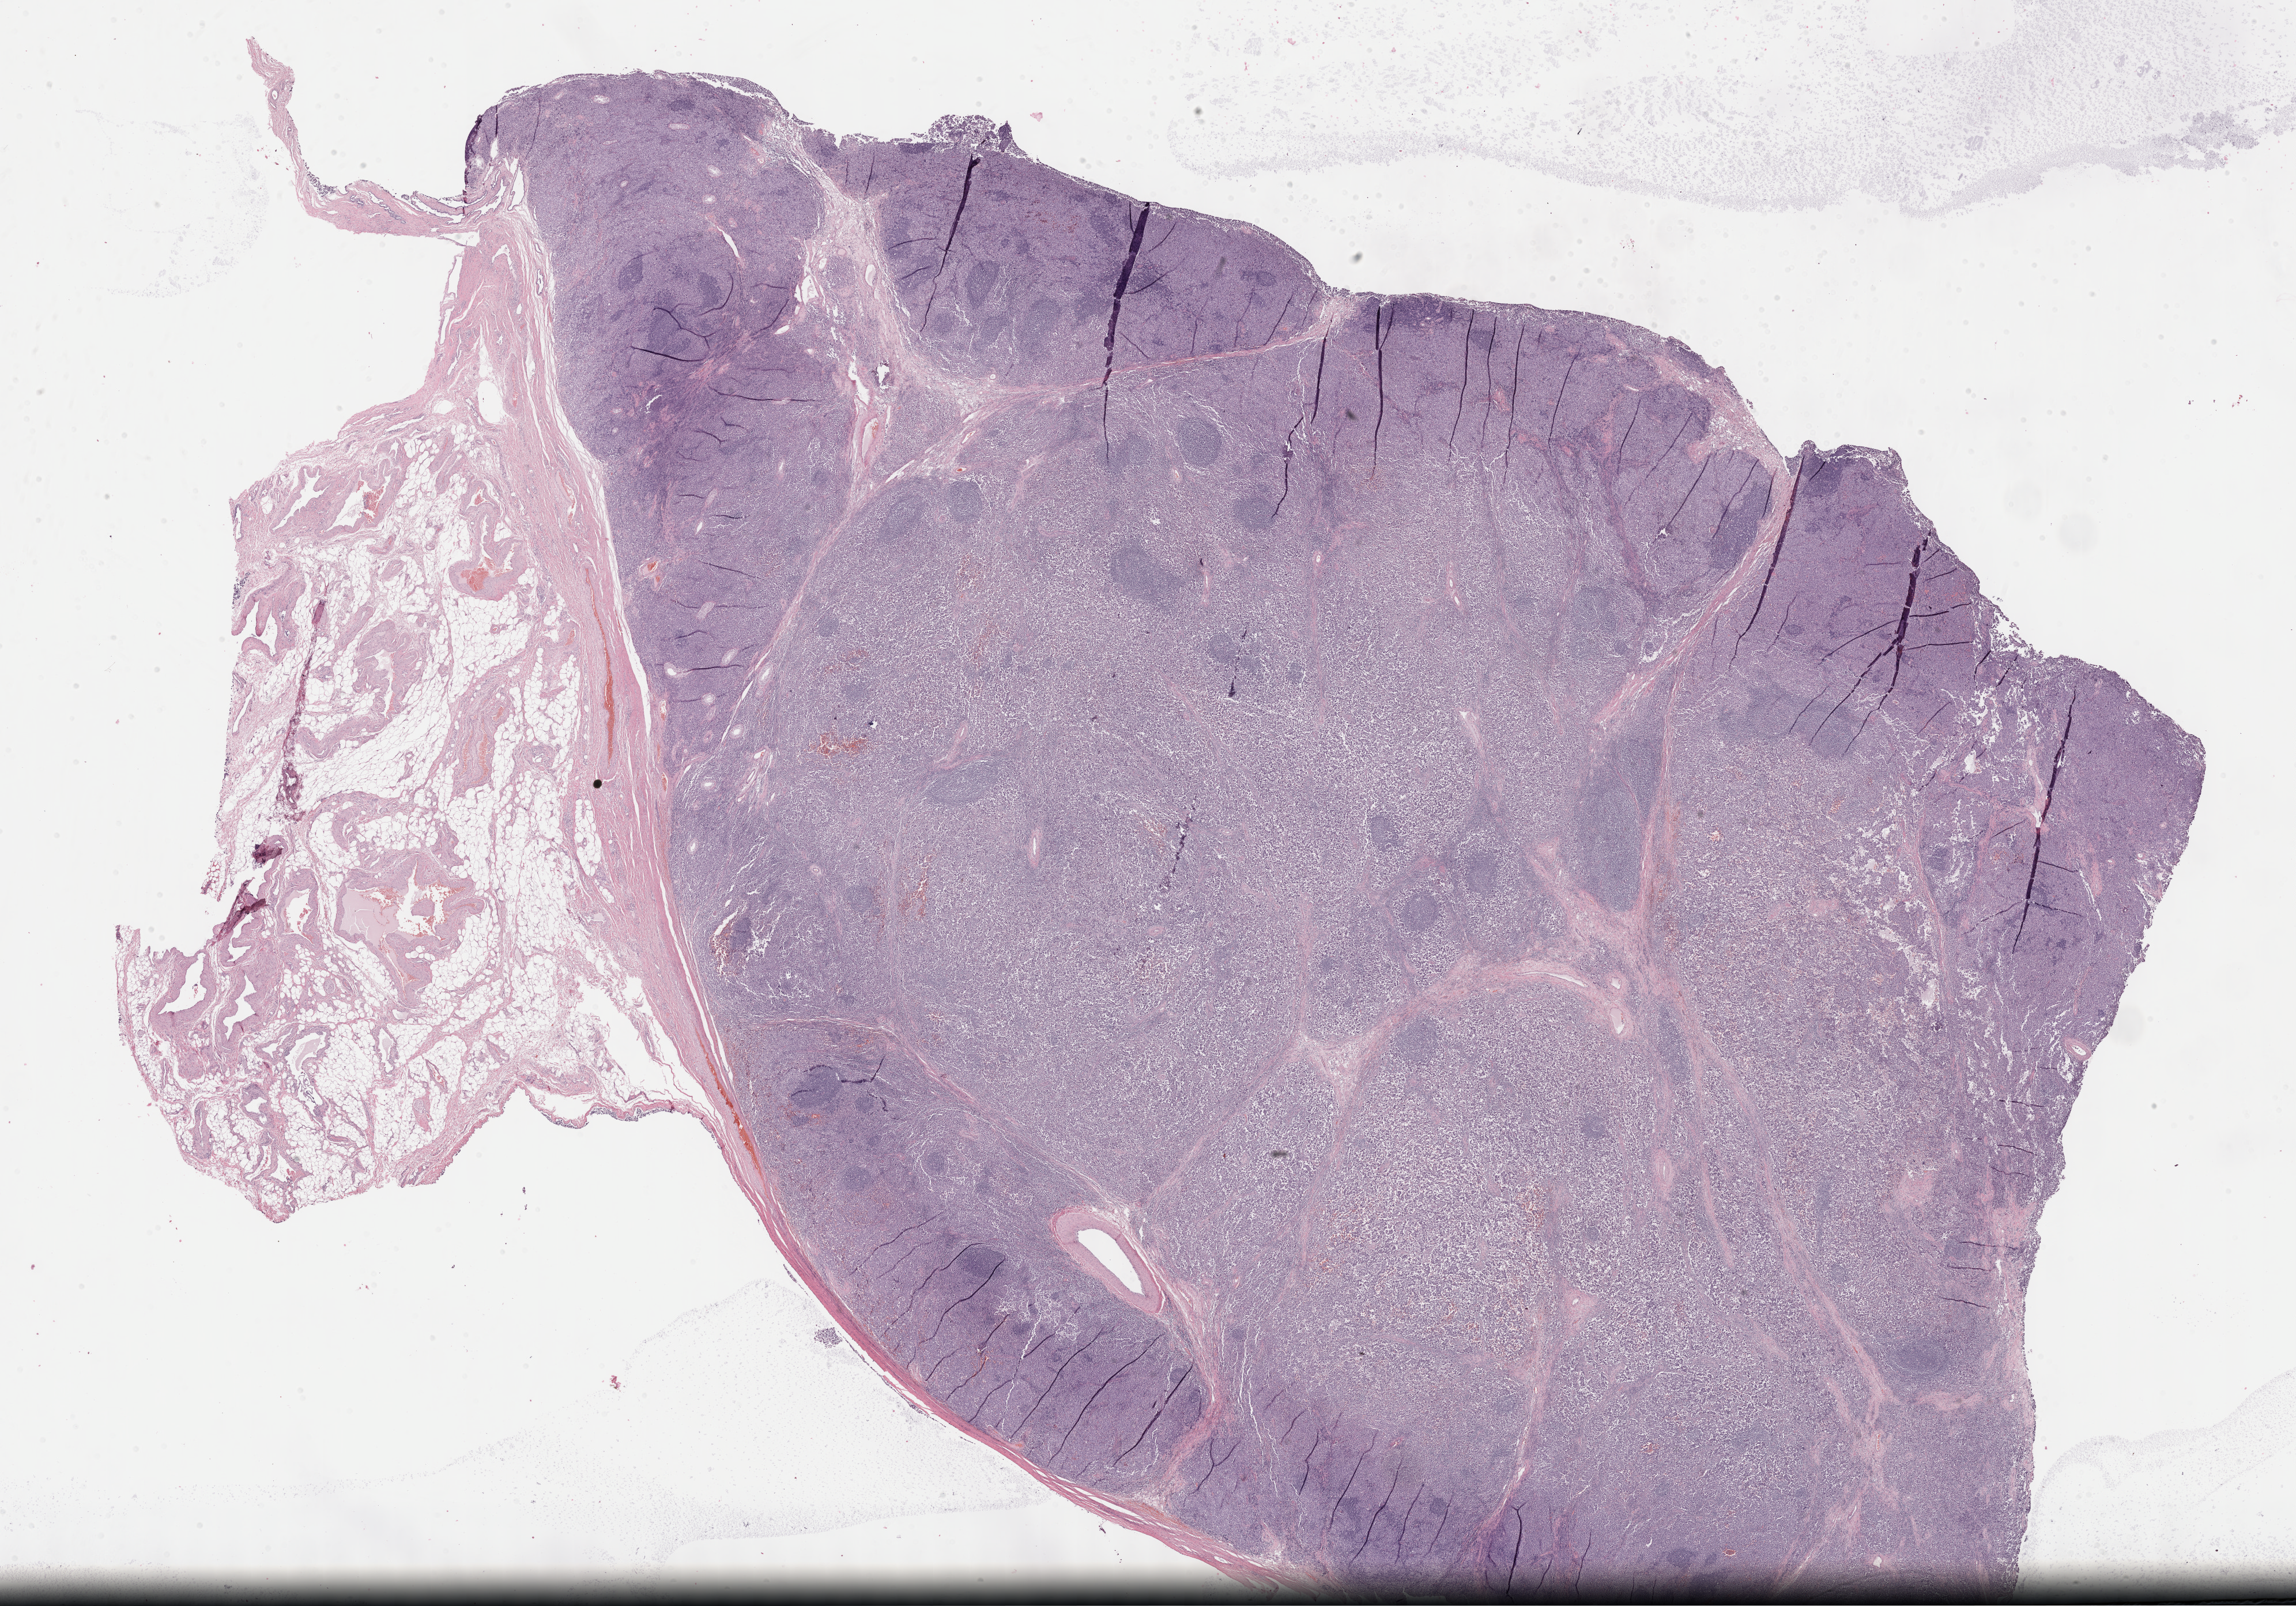
H&E-stained whole-slide image, shown as a low-resolution overview of the whole scanned area (about 32.2 x 22.5 mm, acquisition: 40x scan). Formalin-fixed paraffin-embedded (FFPE) diagnostic section. Primary tumour sample from the testis. Male, age 39 years at initial diagnosis.
AJCC pathologic stage: IA (7th edition). Pathologic diagnosis: Seminoma, NOS. Laterality: right.